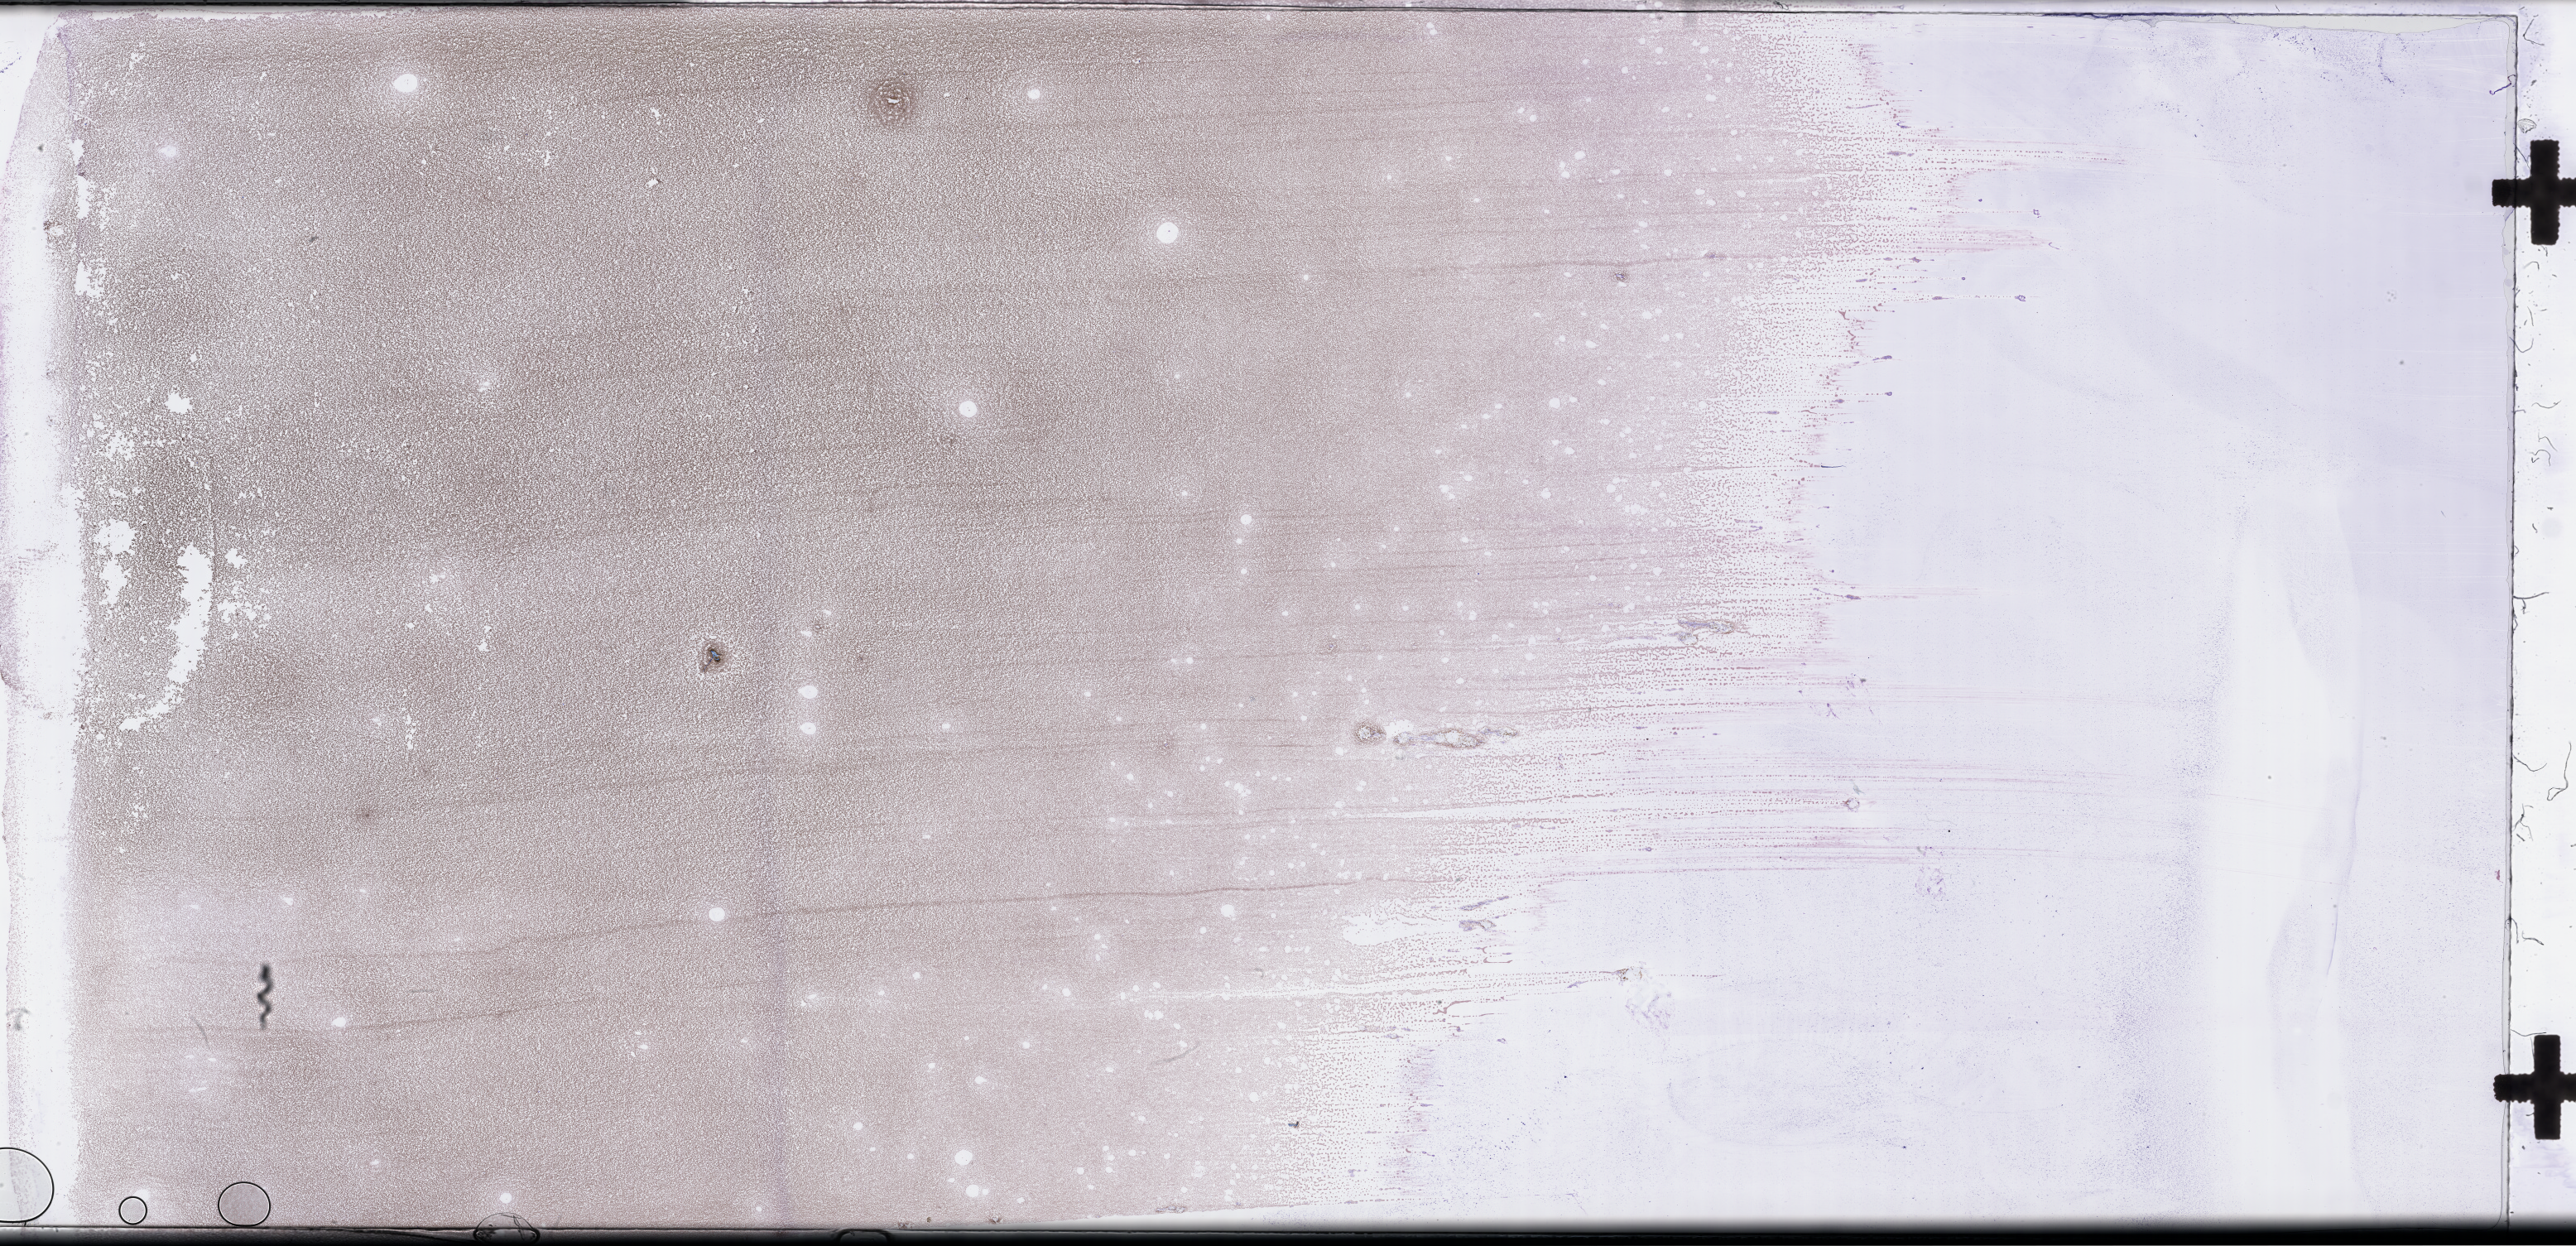
Wright–Giemsa-stained bone marrow smear, whole-slide image — a low-resolution overview of the entire scanned area, about 50.3 x 24.3 mm; specimen time point: collected at baseline (before treatment). Patient: female.
Patient diagnosis: Acute Myeloid Leukemia Not Otherwise Specified.